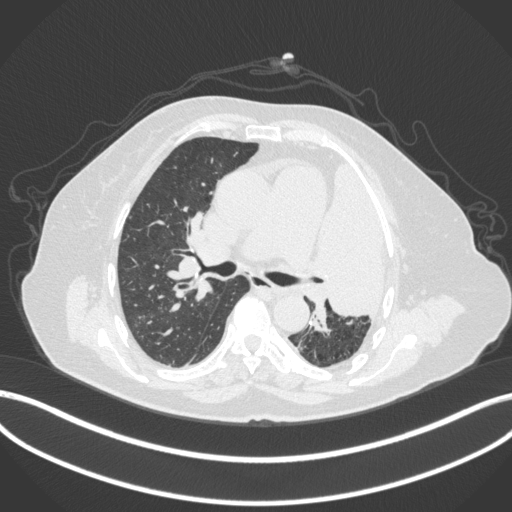
Chest CT, one axial slice; slice 236 of 399 in the series (ordered by position); reconstruction kernel B31f; lung window (W 1500 / L -600 HU); 512 × 512 image matrix, field of view 400 × 400 mm. Female patient, age 75 years. Case-level facts recorded for this patient, not image findings: clinical TNM (as recorded): T3 N3 M1.
Outlined on this slice (rectangle marked by the reading radiologist):
- lung tumour (recorded histology: adenocarcinoma): box from (x=320, y=152) to (x=396, y=325) px